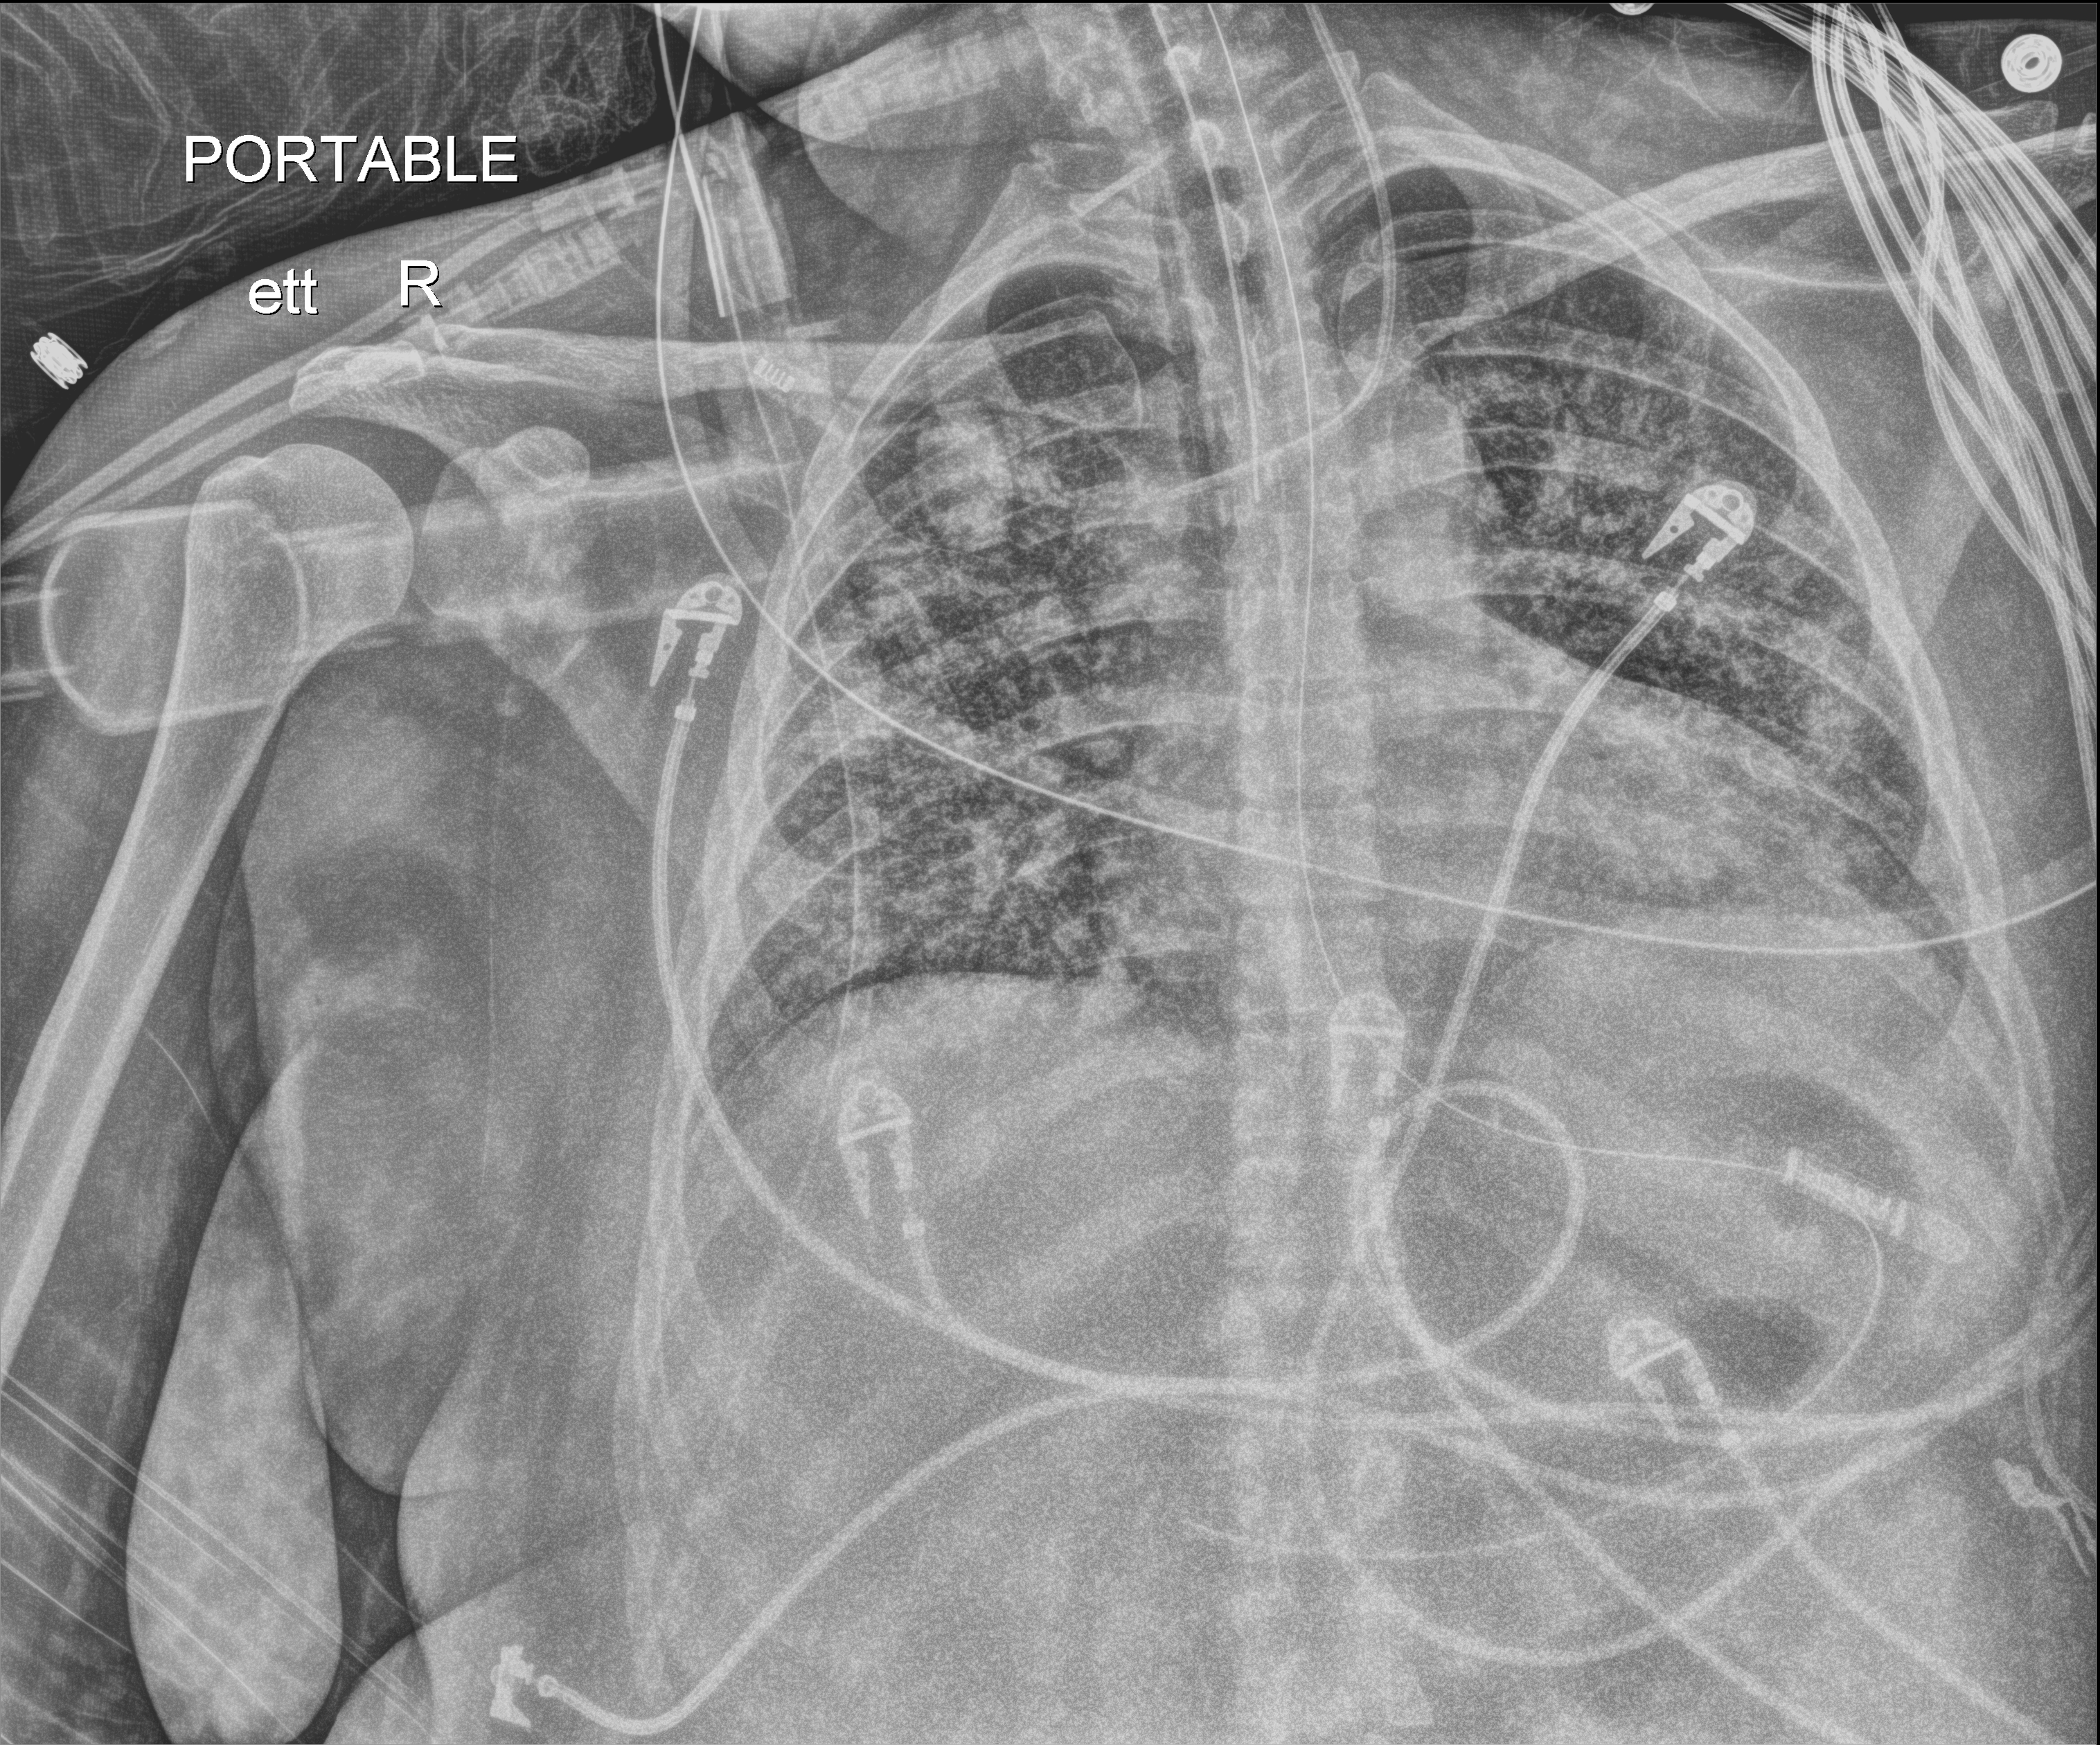
Portable chest radiograph; anteroposterior (AP) projection. Patient hospitalised with COVID-19; female, aged 18–59 years.
Admission-level facts for this patient (not findings on this image; timing relative to this image not recorded):
- mechanically ventilated during this hospital stay: yes